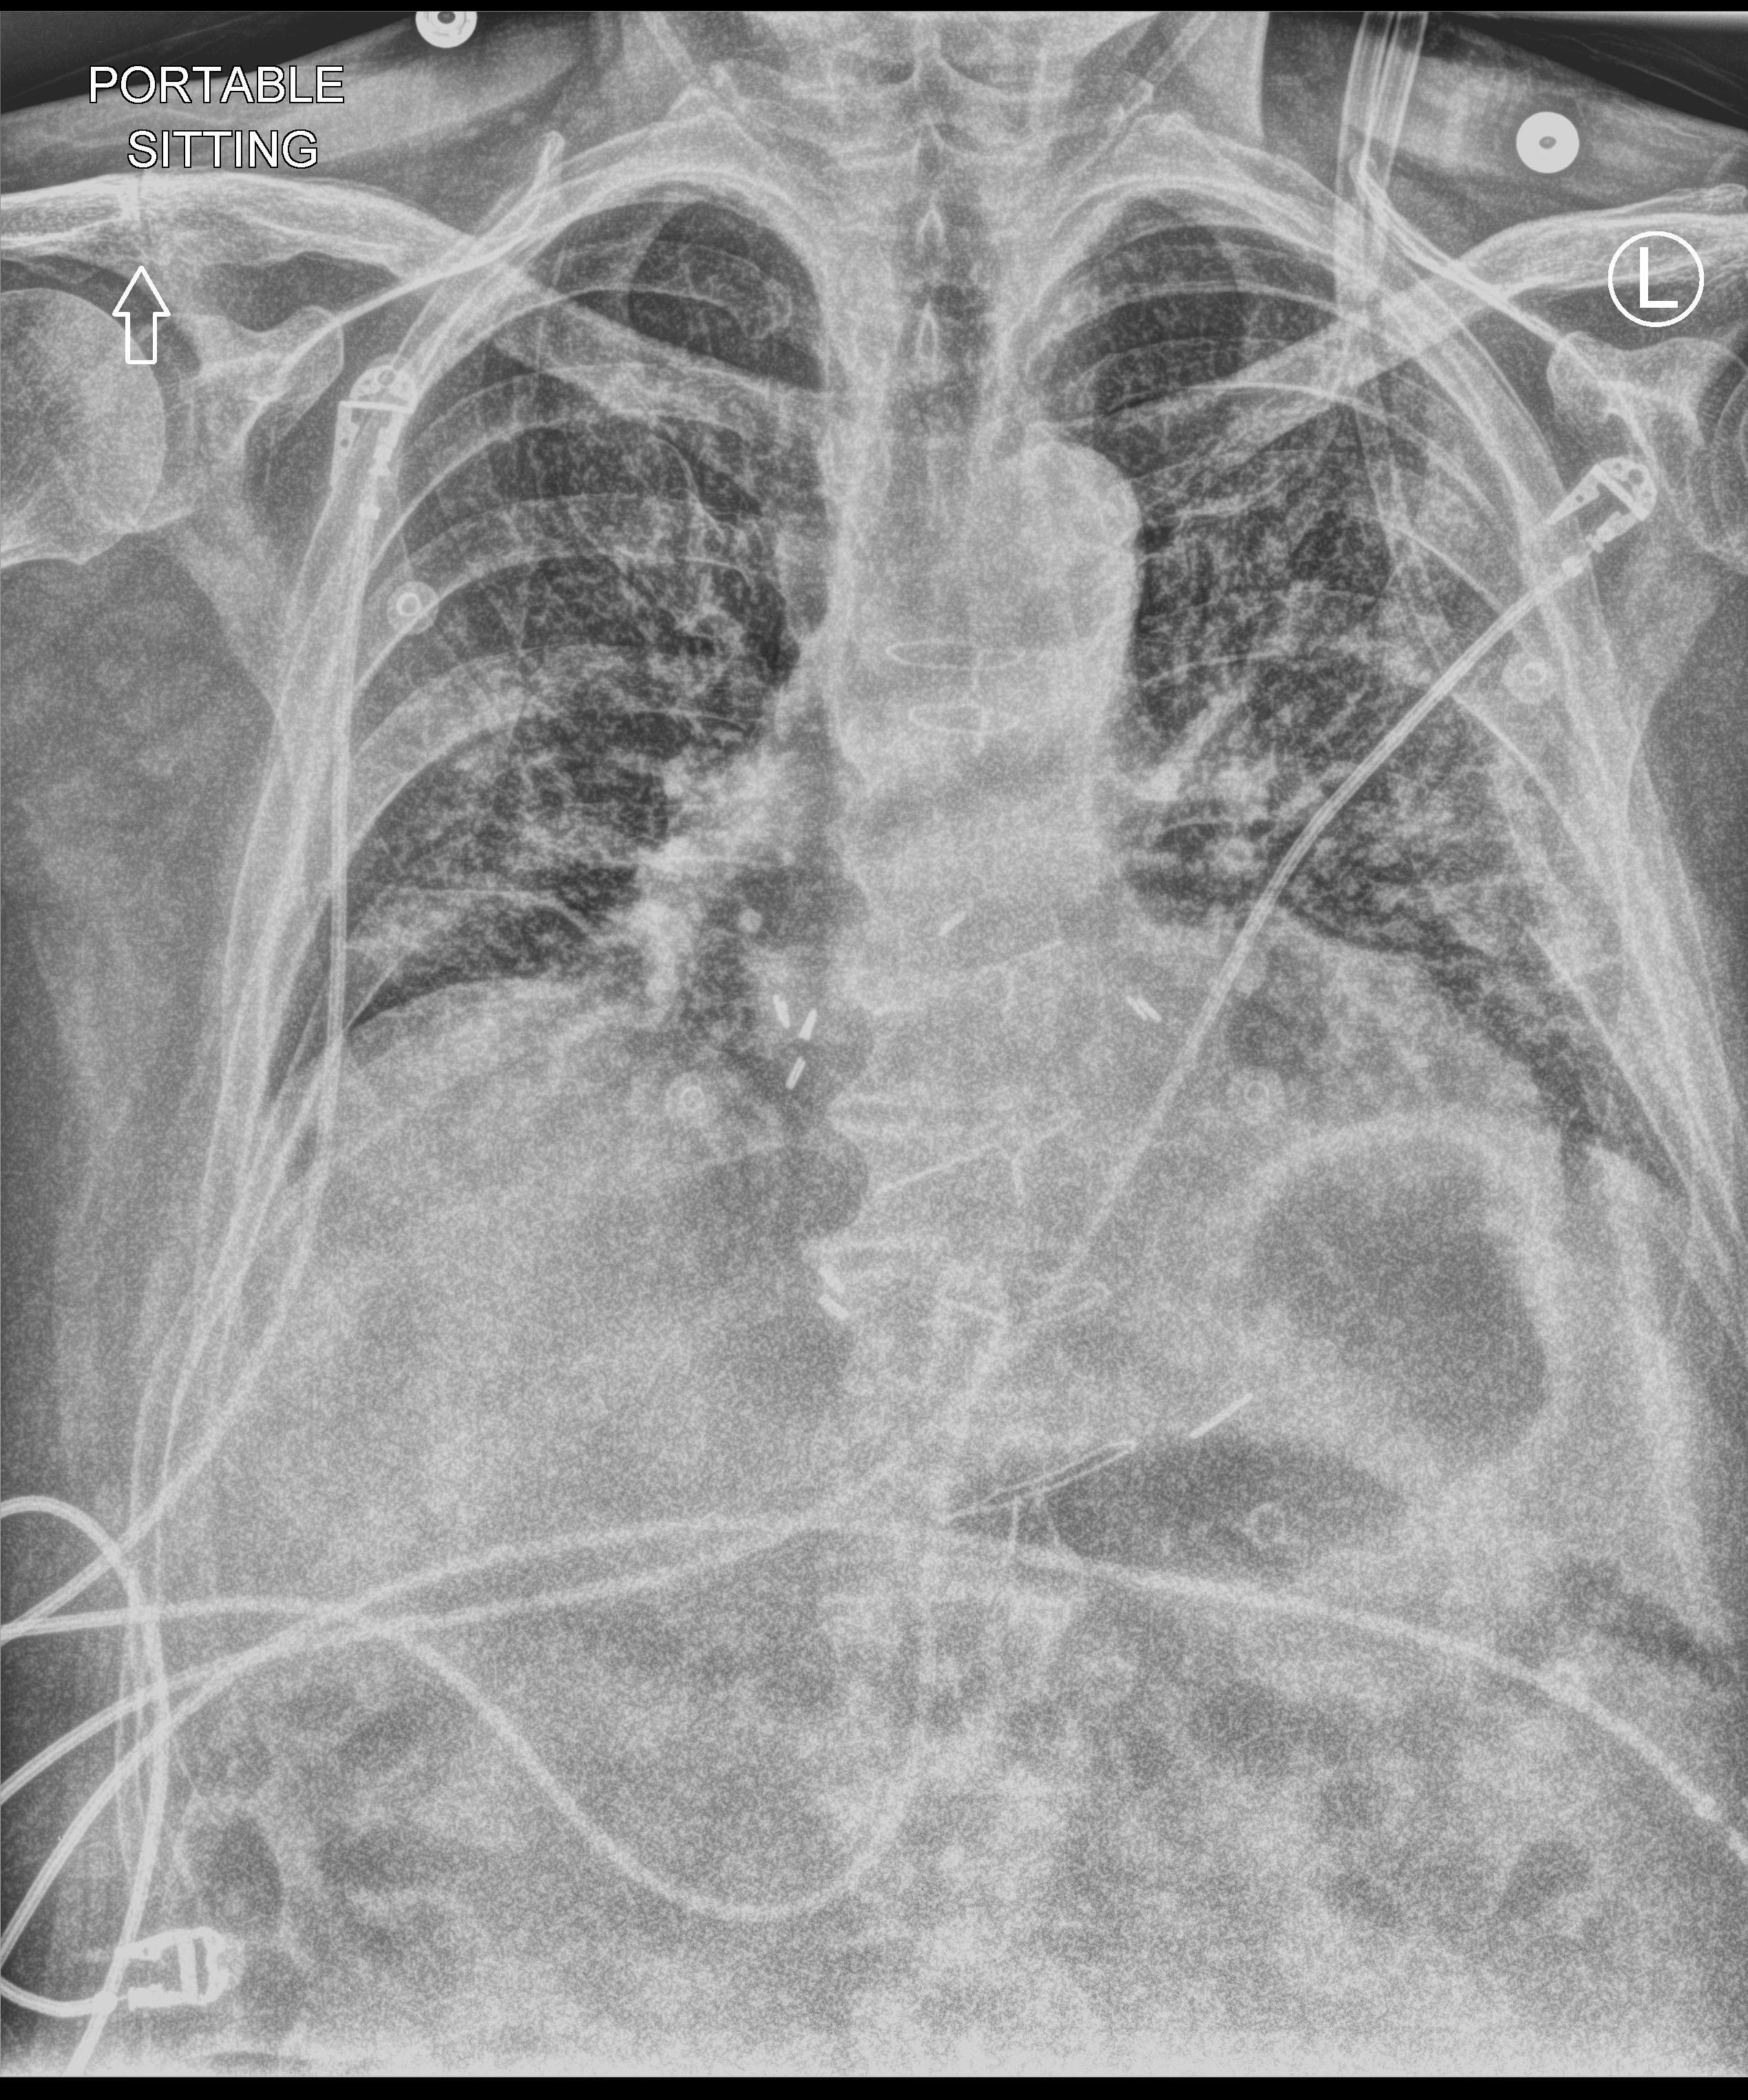
Bedside chest radiograph (computed radiography), anteroposterior (AP) projection. Patient hospitalised with COVID-19; male, aged 75–90 years.
From the hospital-stay record, not from the radiograph (when in the stay this image was taken is not recorded): mechanically ventilated during this hospital stay: no; admitted to intensive care during this hospital stay: no.